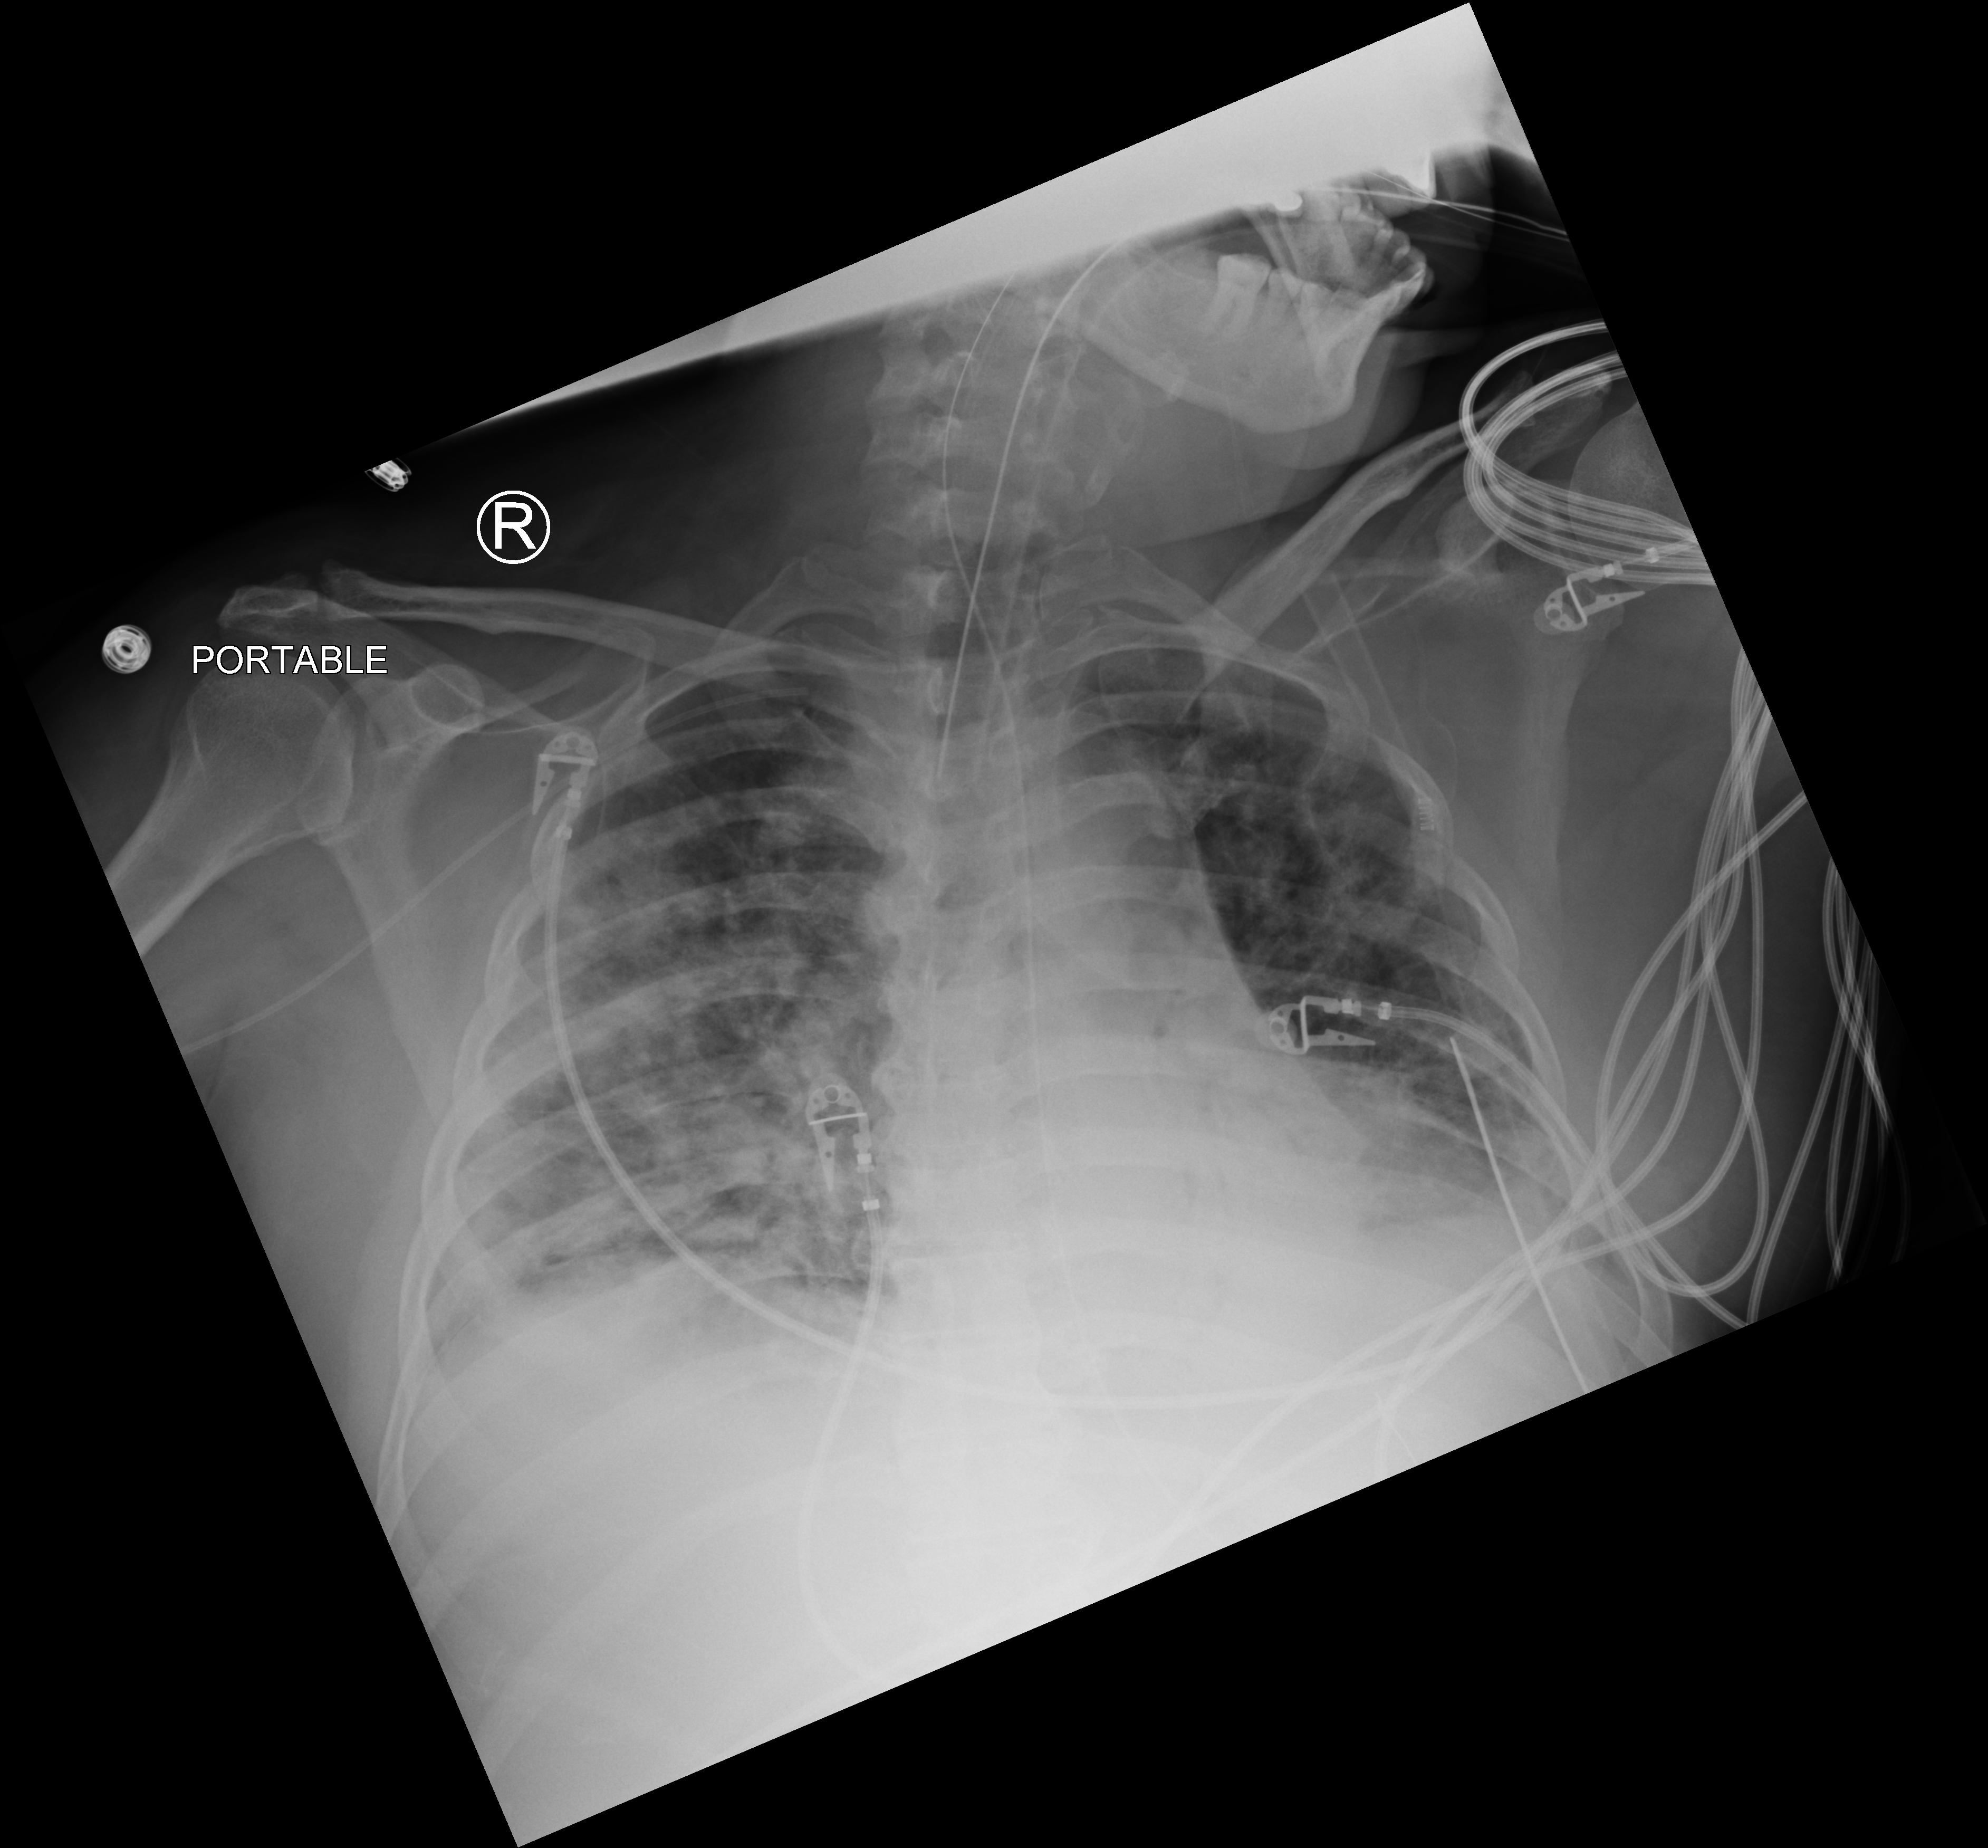
Chest X-ray (portable), anteroposterior (AP) projection. Male patient hospitalised with COVID-19, age 18–59 years.
From the hospital-stay record, not from the radiograph (when in the stay this image was taken is not recorded): hypertension (admission record): yes; COPD (admission record): no.